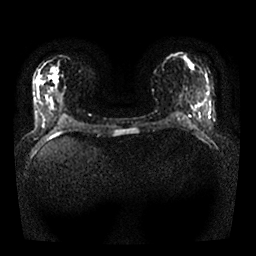
Breast MRI, one axial slice; position 12 of 25 along the scan axis; diffusion-weighted series; image 2 of 4 stored at this slice position (different b-values; order by instance number); 1.5 T; 4 mm slice thickness; 256 × 256 image matrix, field of view 330 × 330 mm. Female patient.
Structures marked on this image (manually delineated by an expert):
- tumour on diffusion-weighted imaging: bounding box <54,77,57,83> (left, top, right, bottom; pixels)